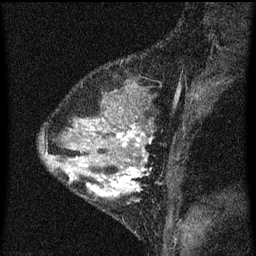
Breast MRI (dynamic contrast-enhanced), one sagittal slice; dynamic contrast-enhanced series, image 2 of 3 at this slice position (ordered by acquisition); 1.5 T; TE 4.2 ms, TR 8 ms; 2 mm slice thickness; 256 × 256 image matrix. Patient: female, 33 years.
Outlined on this slice (semi-automatic segmentation, software-assisted and operator-edited):
- analysis volume of interest (the breast-tissue region the enhancement analysis was run in; not a lesion): bounding box (x1, y1, x2, y2) in pixels: (67, 118, 153, 211)
- tumour enhancement mask (voxels above the 70 % enhancement threshold inside the analysis volume of interest): (76, 124, 152, 197)